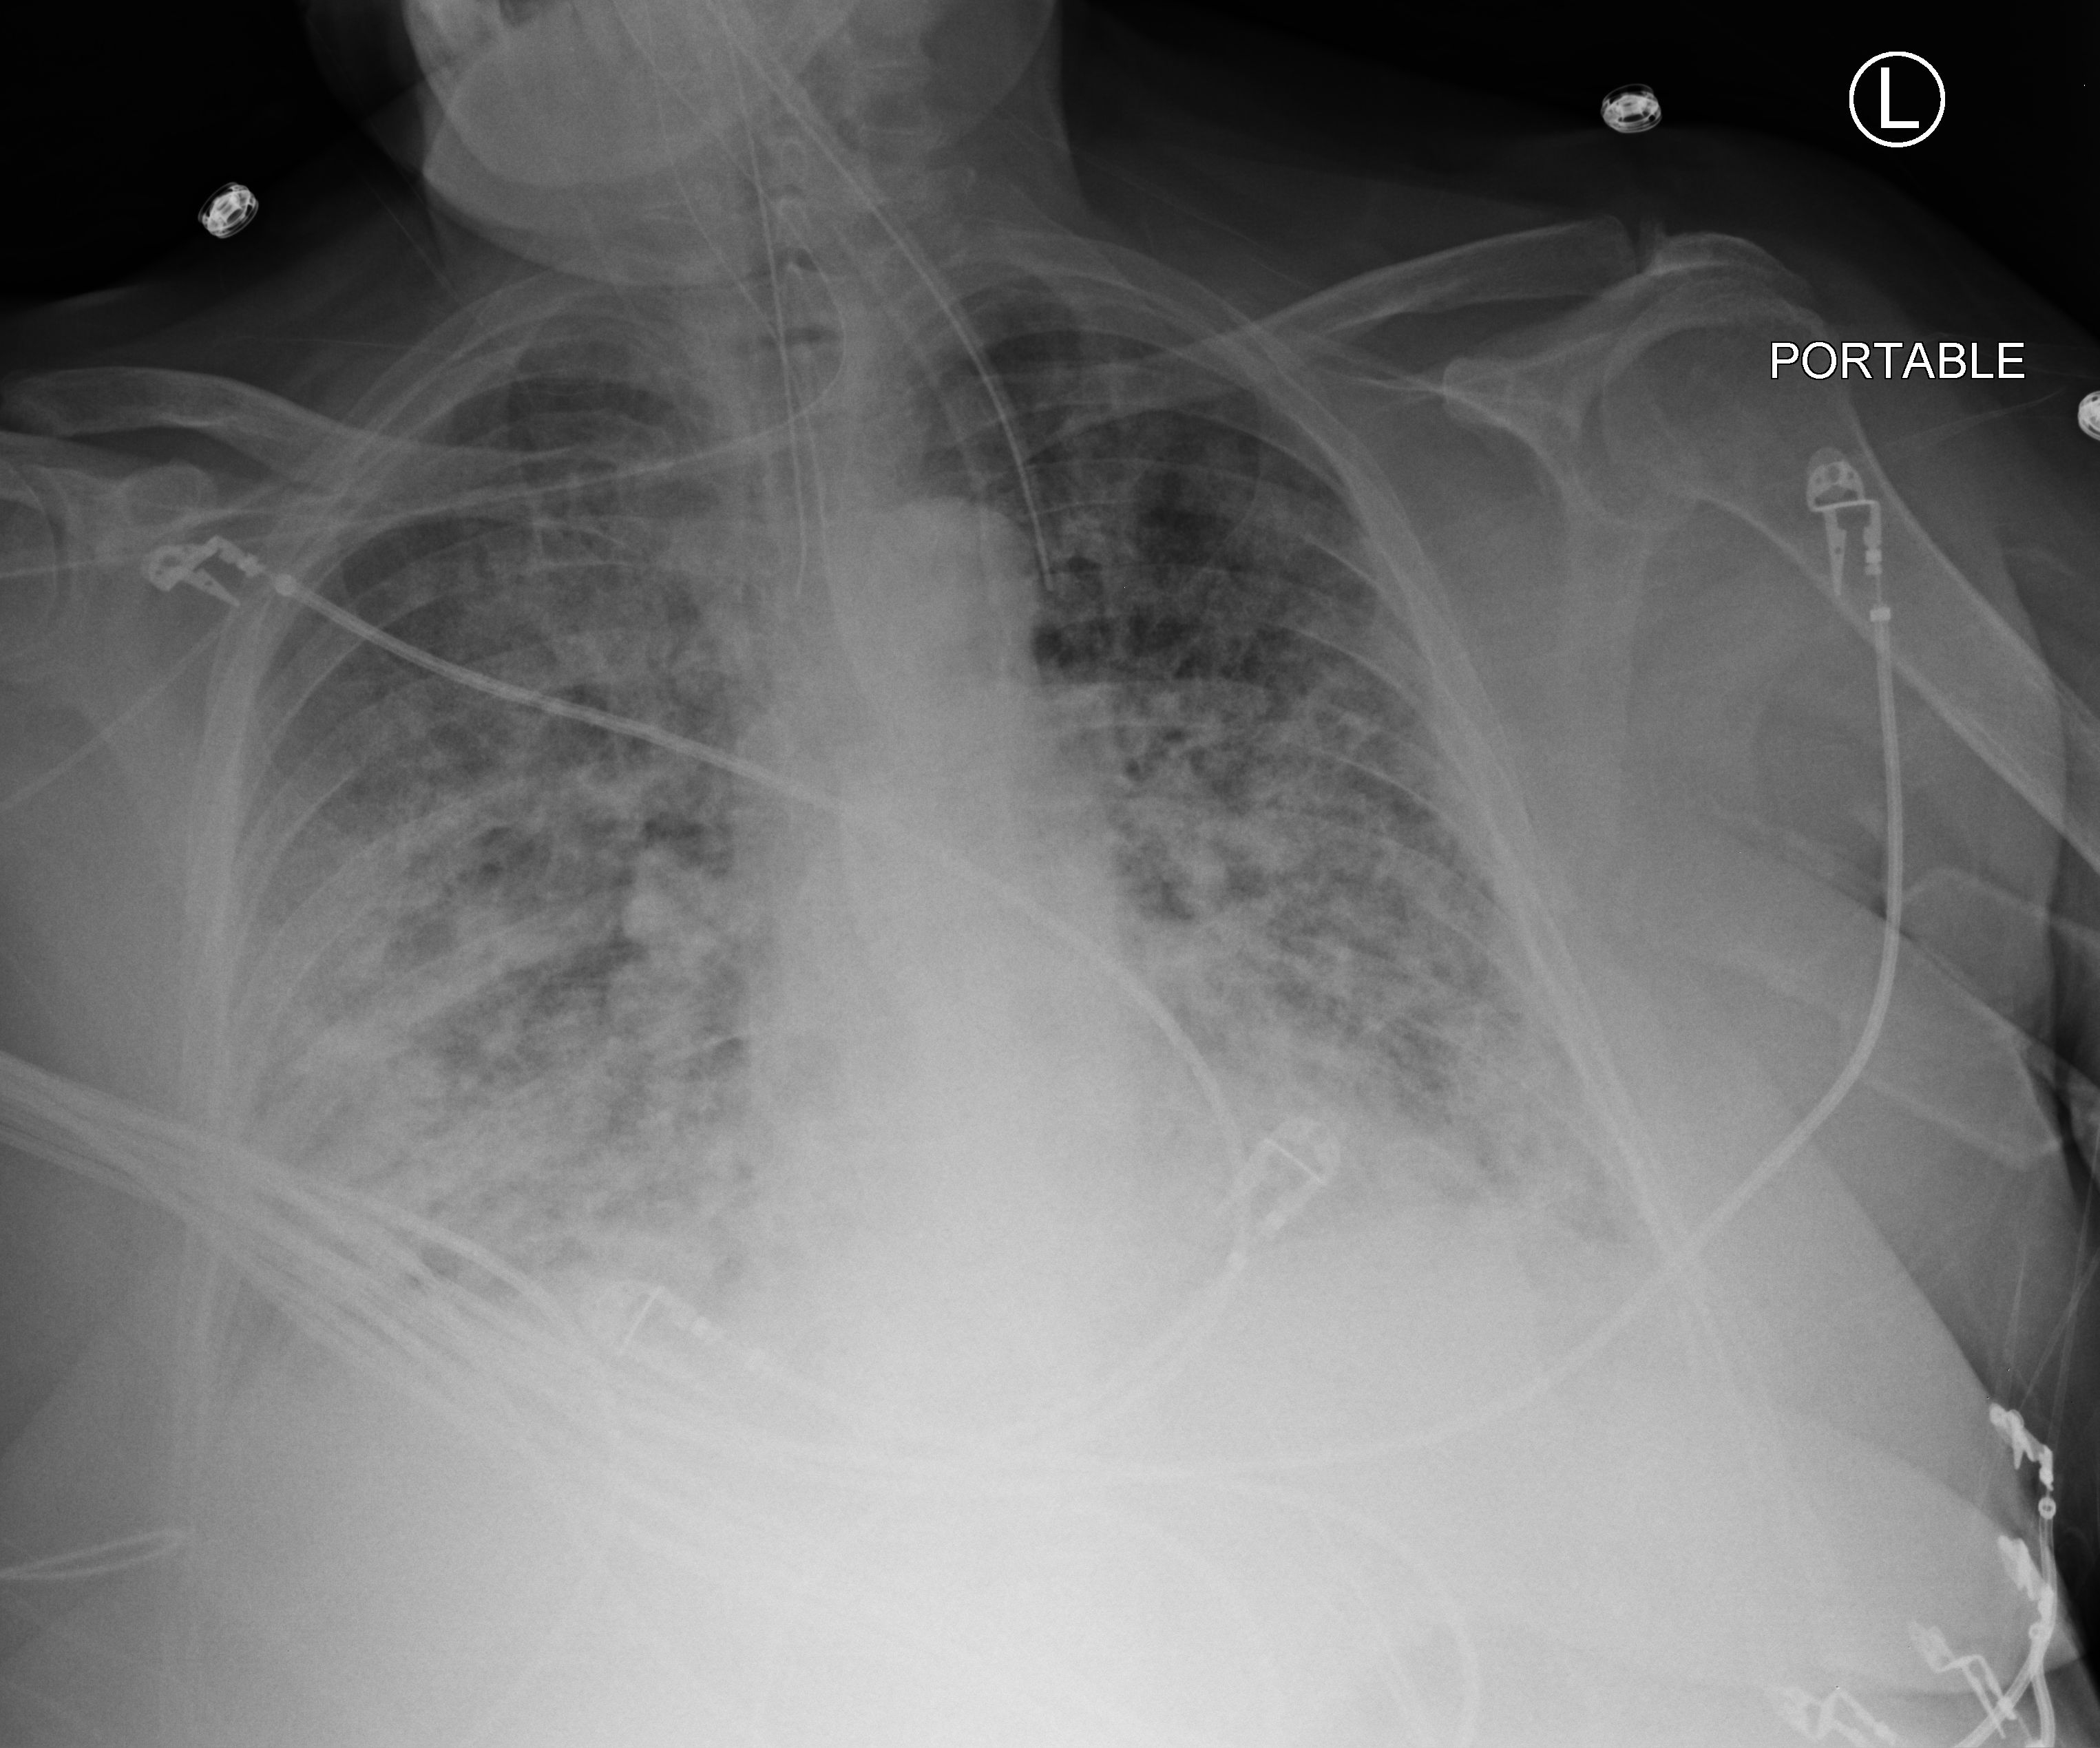
Bedside chest radiograph (computed radiography); anteroposterior (AP) projection. Female patient hospitalised with COVID-19, age 60–74 years.
Hospital-stay facts (about this admission, not read from this image; timing relative to this image not recorded): hypertension (admission record): yes.